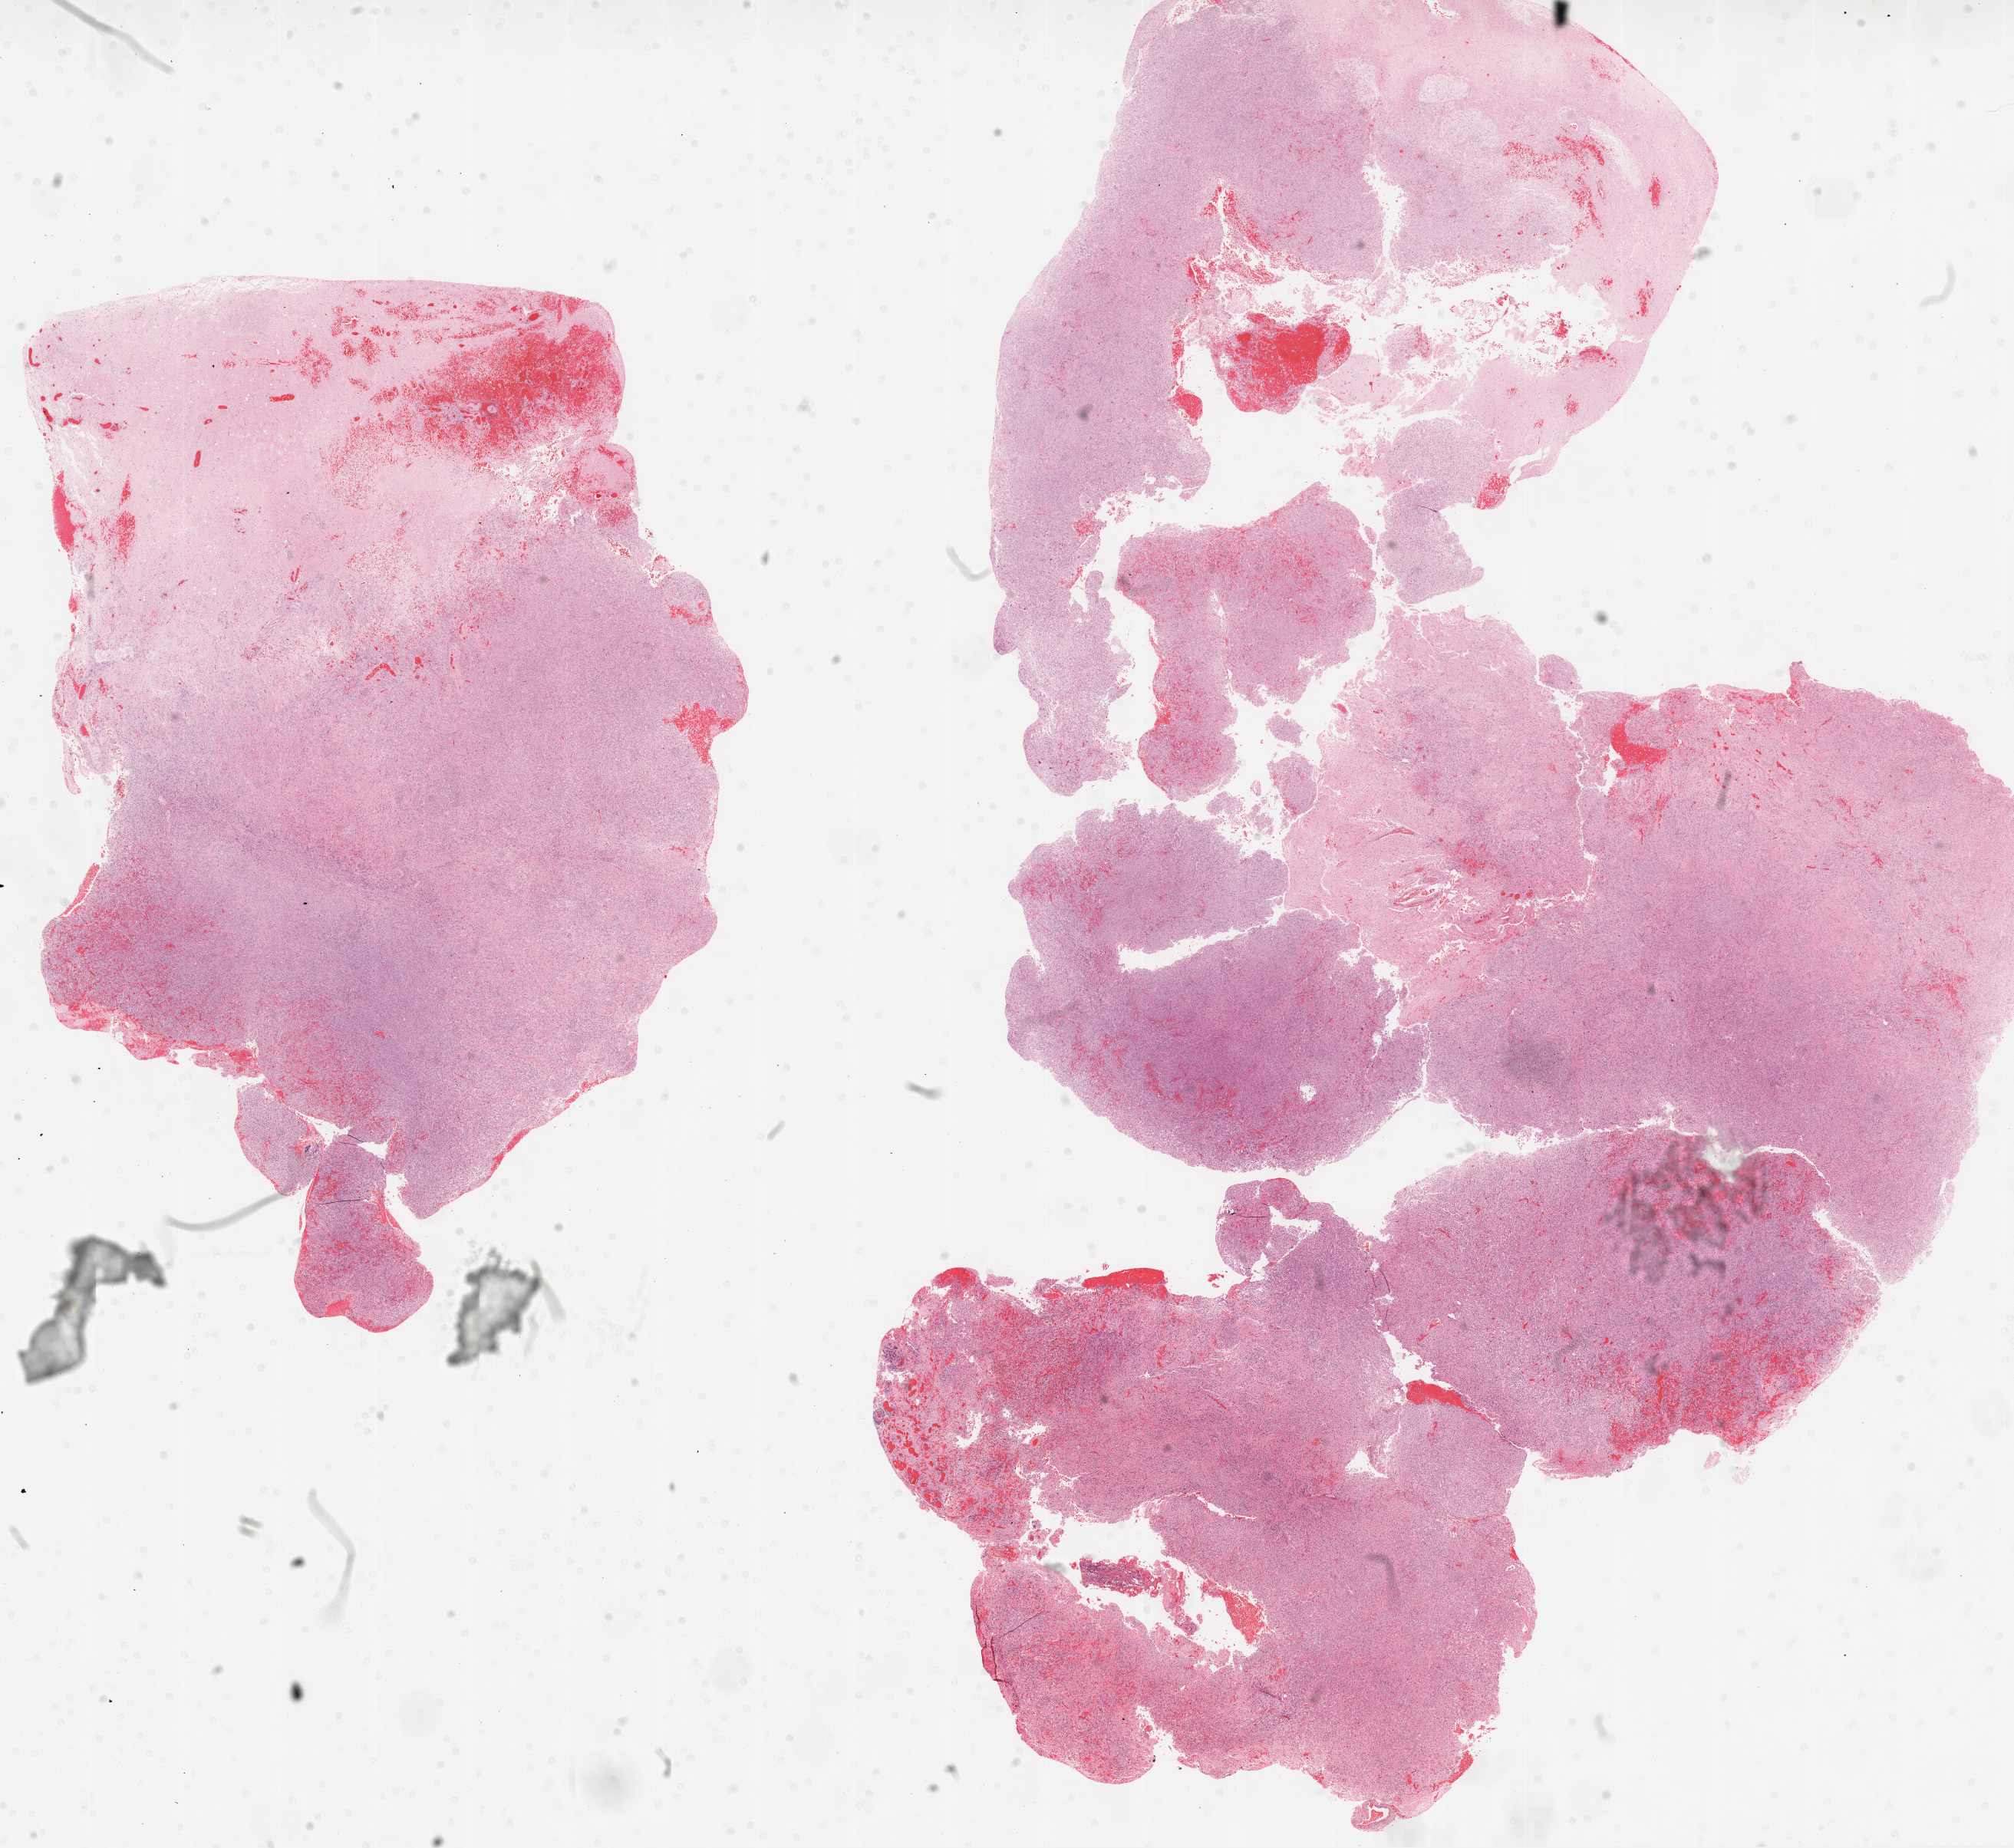
Digitized Hematoxylin and eosin (H&E) stained tissue section (whole slide) — a low-resolution overview of the entire scanned area, about 21.1 x 19.3 mm. FFPE section. Brain, primary tumour sample. Male patient; age at initial diagnosis 47 years.
Diagnosis: Glioblastoma.